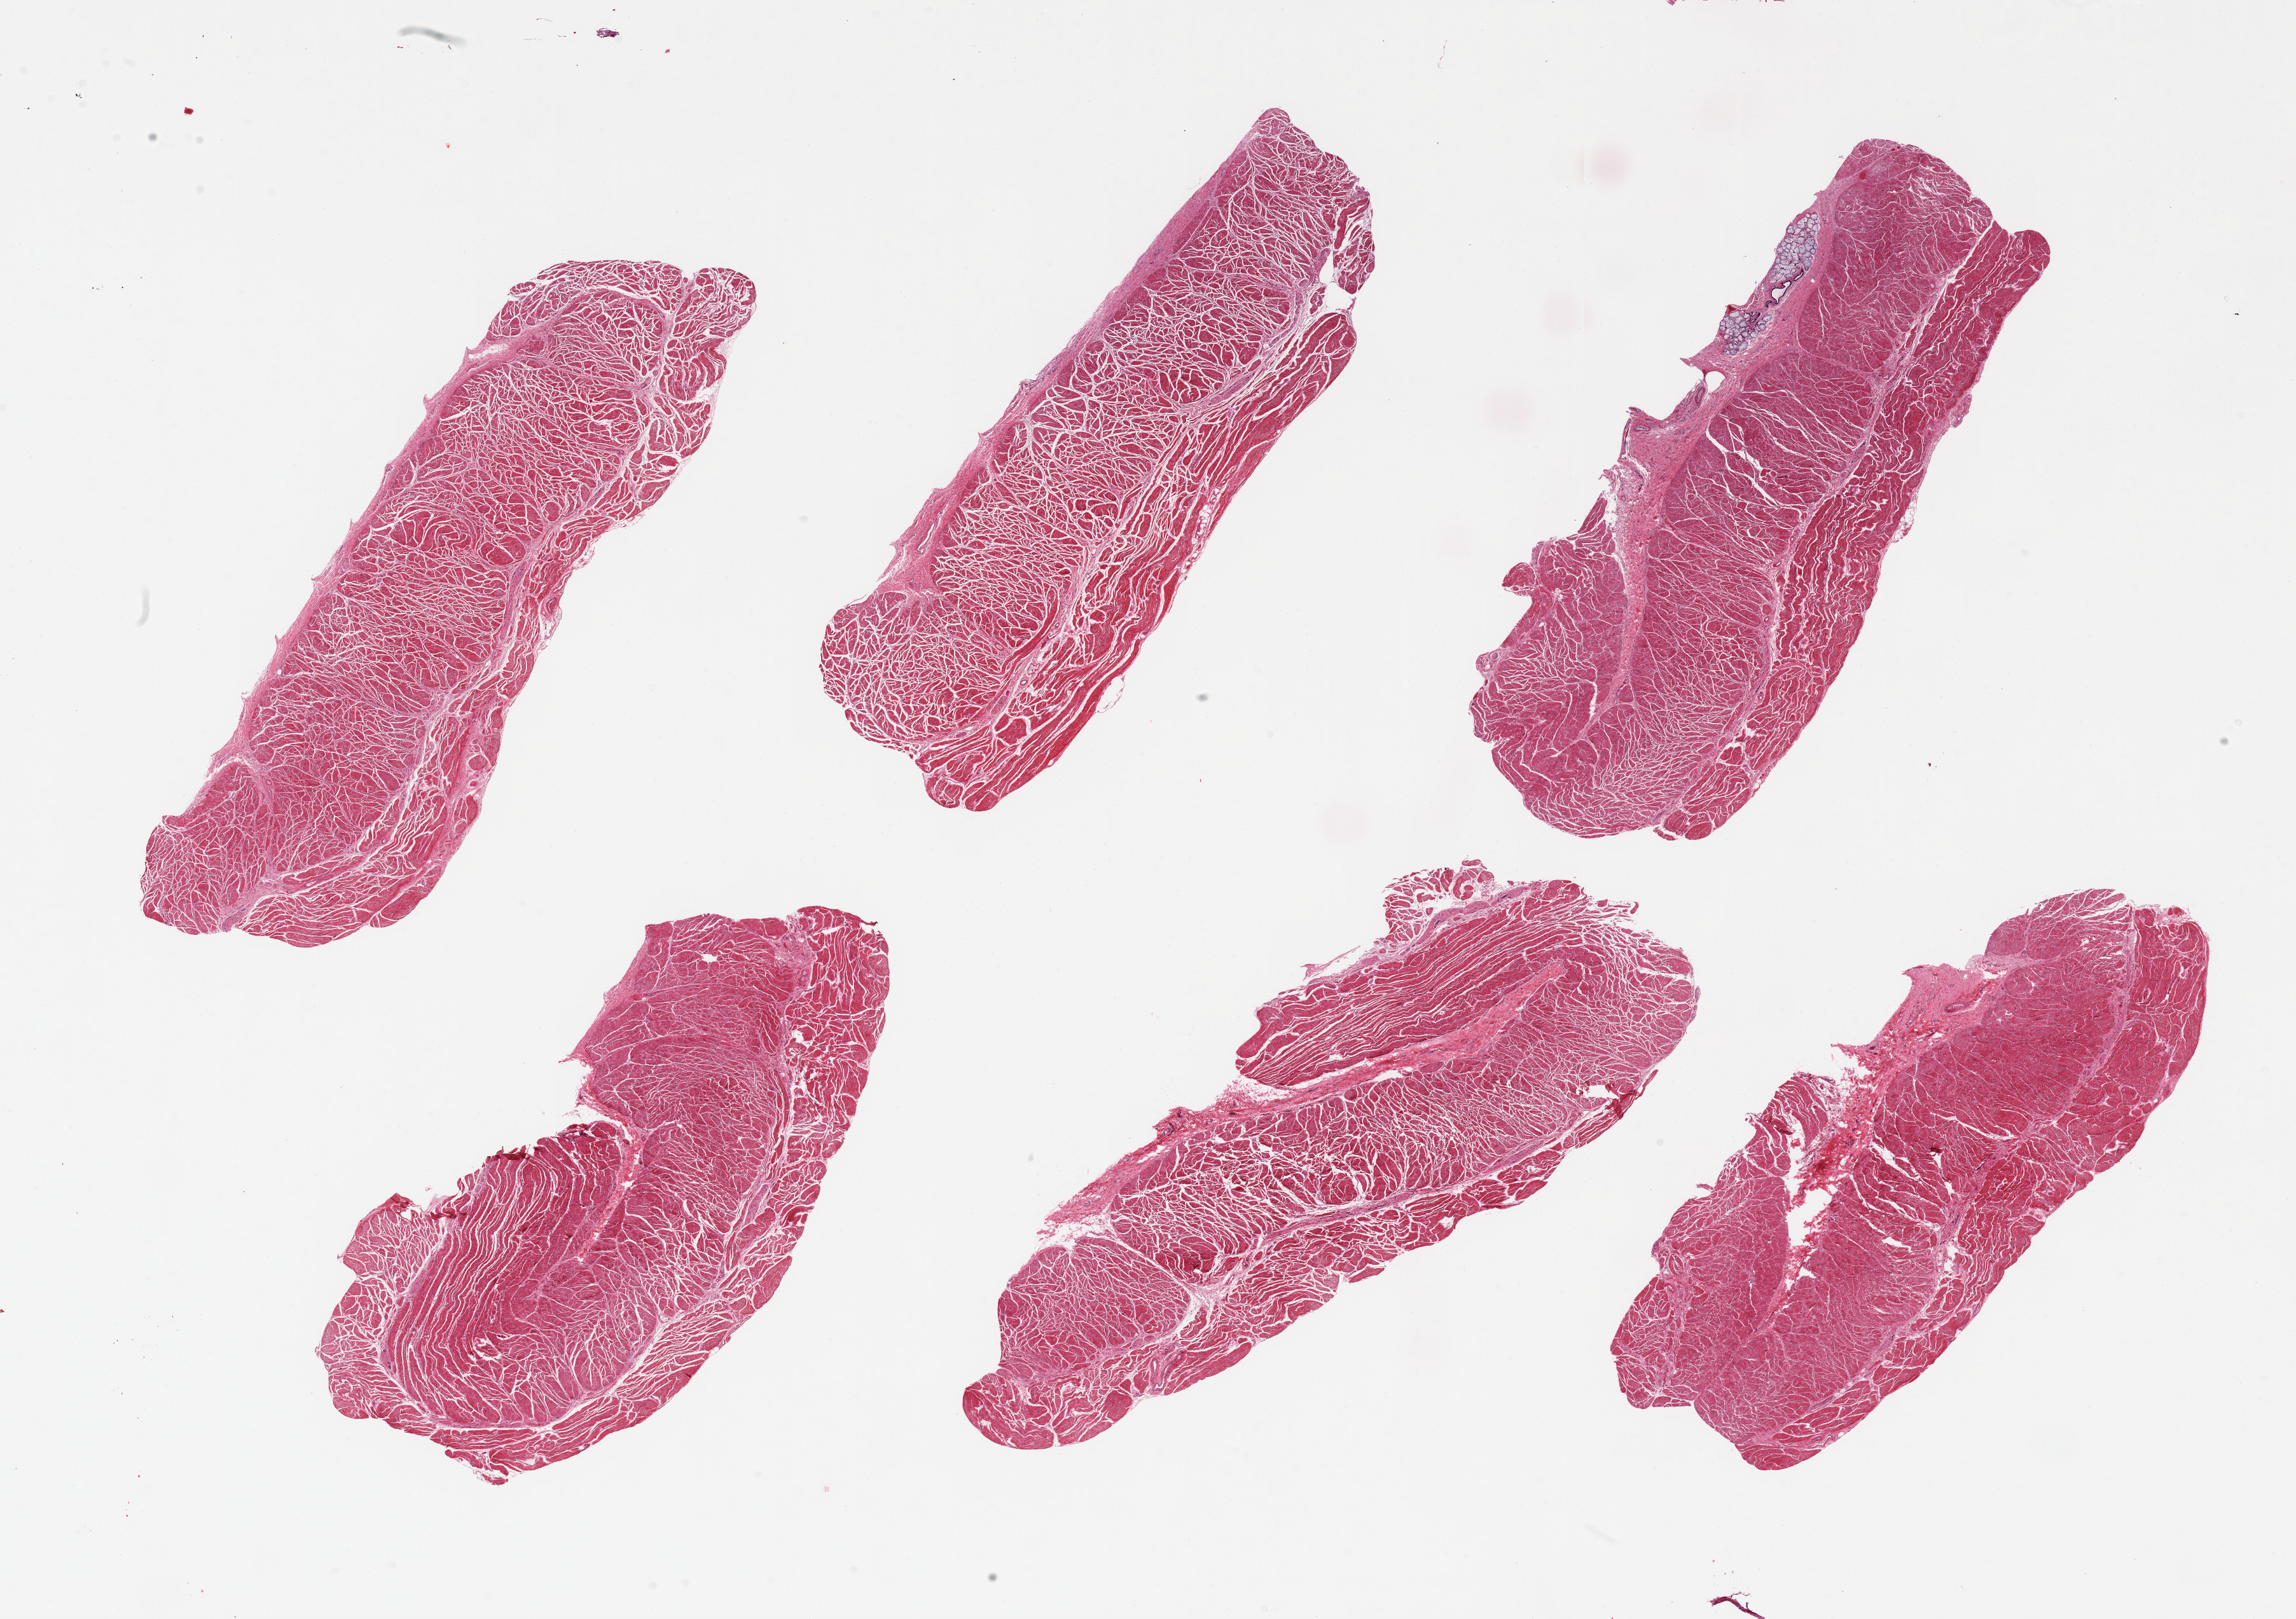
Haematoxylin and eosin whole-slide image, brightfield, low-resolution overview of the scanned area, about 28.5 x 20.1 mm, PAXgene-fixed, paraffin-embedded tissue, target tissue: gastroesophageal junction, donor tissue sample.
• review note (as recorded): 6 pieces; target muscularis; small focus of submucosal gland